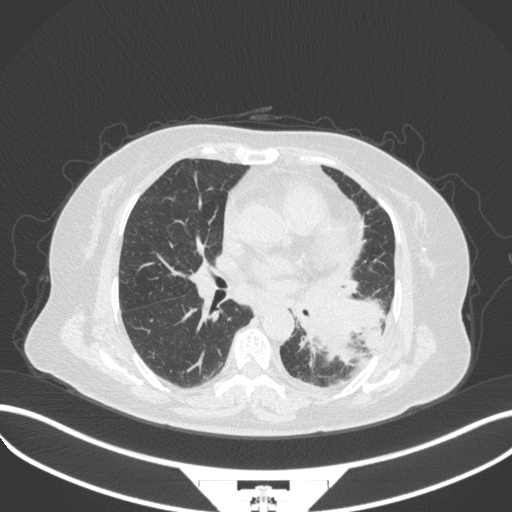
Chest CT, one axial slice; reconstruction kernel B31f; lung window (W 1500 / L -600 HU); 1 mm slice thickness; 512 × 512 image matrix, field of view 400 × 400 mm. Patient: female, 69 years. Case-level facts recorded for this patient, not image findings: clinical TNM (as recorded): T2b N3 M1.
Outlined on this slice (bounding box drawn by a radiologist):
- lung tumour (recorded histology: adenocarcinoma): bounding box (x1, y1, x2, y2) in pixels: (297, 286, 387, 366)